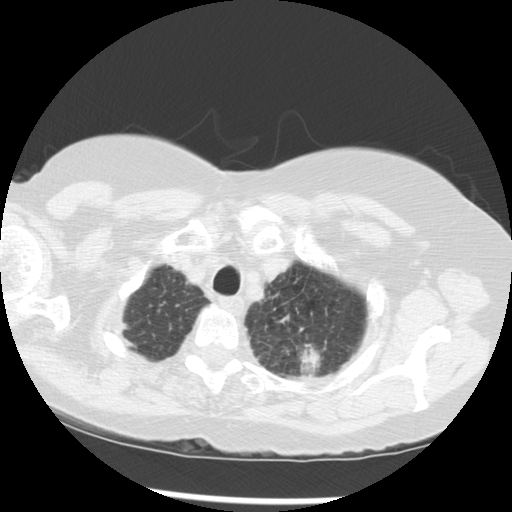
Low-dose screening chest CT, axial slice, third screening round (two years after baseline), lung window (W 1500 / L -600 HU), 2.5 mm slice thickness, standard (soft-tissue) reconstruction kernel (STANDARD), slice 248 of 283 in the series, 512 × 512 image matrix, field of view 330 × 330 mm. Female, age 70 years at enrolment.
Expert reader's lesion annotation, bounding box (x1, y1, x2, y2) in pixels: (243, 296, 343, 383). Reader record for this screening exam (exam-level; its link to the box is not recorded): non-calcified nodule or mass ≥4 mm, left upper lobe, 32 × 26 mm, spiculated (stellate) margins, soft tissue attenuation, pre-existing on the prior screen: yes; interval growth: yes. Official screen result: positive, other. Later outcome: lung cancer diagnosed 24 days after this screen — neoplasm, malignant, left upper lobe, stage IIIB (AJCC 6th edition), 40 mm at pathology.